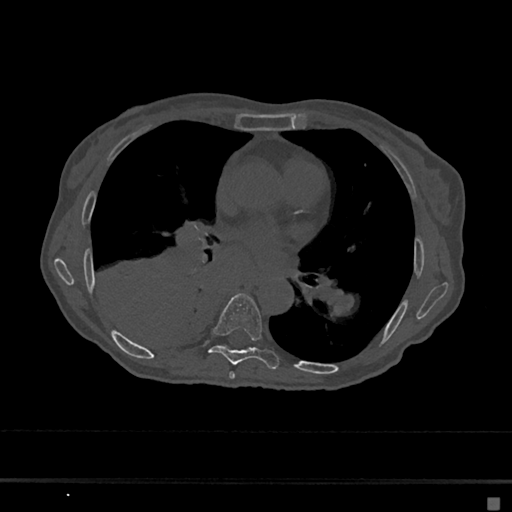
CT including the spine, one axial slice. Position 370 of 797 along the scan axis. 120 kVp. Bone window (W 1800 / L 400 HU). 512 × 512 image matrix. Female patient, age 68 years. Case-level facts recorded for this patient, not image findings: primary cancer: renal.
Outlined on this slice (semi-automatically segmented with operator editing):
- T6 vertebra: bounding box [x1, y1, x2, y2] px = [229, 371, 235, 379]
- T7 vertebra: [208, 294, 279, 370]